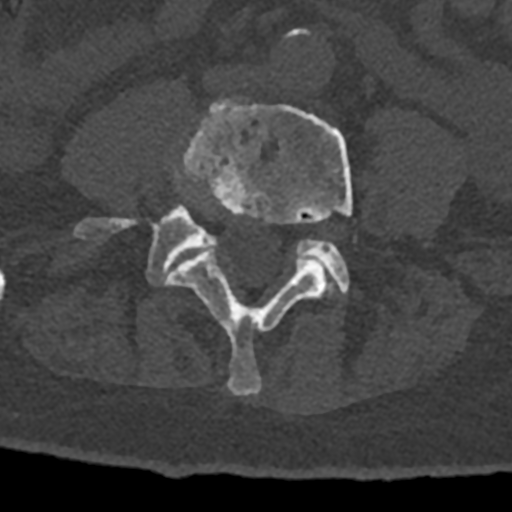
CT including the spine, one axial slice; slice 238 of 797 in the series (ordered by position); 120 kVp; bone window (W 1800 / L 400 HU); 0.5 mm slice thickness; 512 × 512 image matrix. Male patient, age 74 years. From the clinical record (not read from this slice): primary cancer: renal.
Annotated regions visible in this slice (semi-automatic segmentation, software-assisted and operator-edited):
- L4 vertebra: box from (x=166, y=100) to (x=352, y=395) px
- L5 vertebra: (x=74, y=205)–(x=350, y=294)